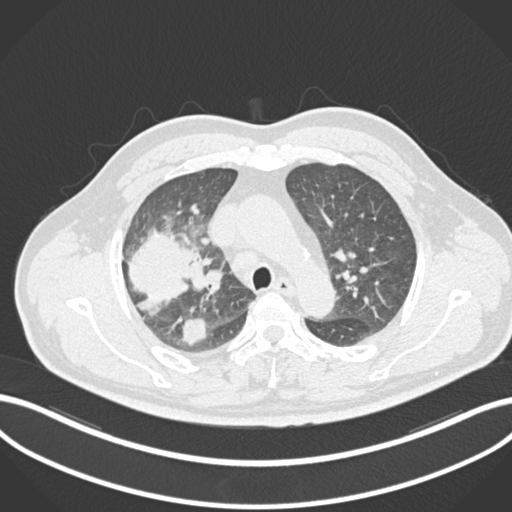
Chest CT, one axial slice. Position 665 of 852 along the scan axis. Lung window (W 1500 / L -600 HU). 1 mm slice thickness. 512 × 512 image matrix, field of view 400 × 400 mm. Male patient, age 55 years. Case-level facts recorded for this patient, not image findings: clinical TNM (as recorded): T3 N2 M1.
Structures marked on this image (rectangle marked by the reading radiologist):
- lung tumour (recorded histology: adenocarcinoma): bounding box [x1, y1, x2, y2] px = [121, 227, 209, 316]